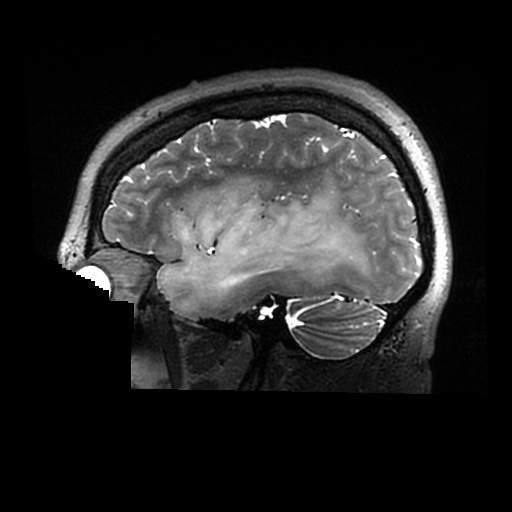
Brain MRI from a brain-tumour surgery series, one sagittal slice. Slice 217 of 320 in the series (ordered by position). 0.6 mm slice thickness. 512 × 512 image matrix. Case-level facts recorded for this patient, not image findings: histopathology: Astrocytoma; WHO grade: 2; IDH mutation: yes.
Annotated regions visible in this slice (outlined manually by an expert reader):
- tumour: bounding box [x1, y1, x2, y2] px = [157, 187, 378, 312]